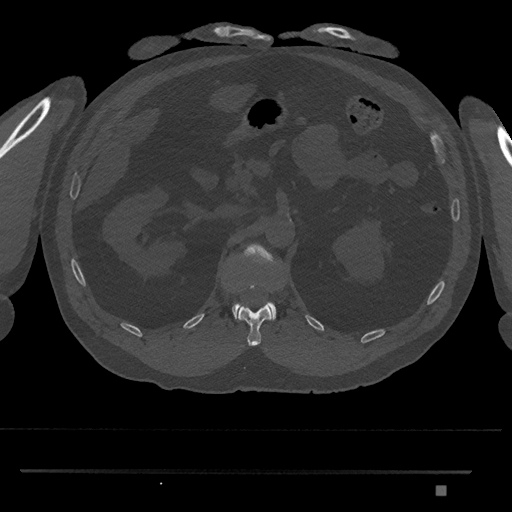
CT including the spine, one axial slice. Position 861 of 1134 along the scan axis. Bone window (W 1800 / L 400 HU). 512 × 512 image matrix, field of view 429 × 429 mm. Patient: male, 65 years. Case-level facts recorded for this patient, not image findings: primary cancer: prostate.
Annotated regions visible in this slice (semi-automatically segmented with operator editing):
- L1 vertebra: bounding box [x1, y1, x2, y2] px = [232, 244, 276, 321]
- T12 vertebra: [238, 305, 272, 346]